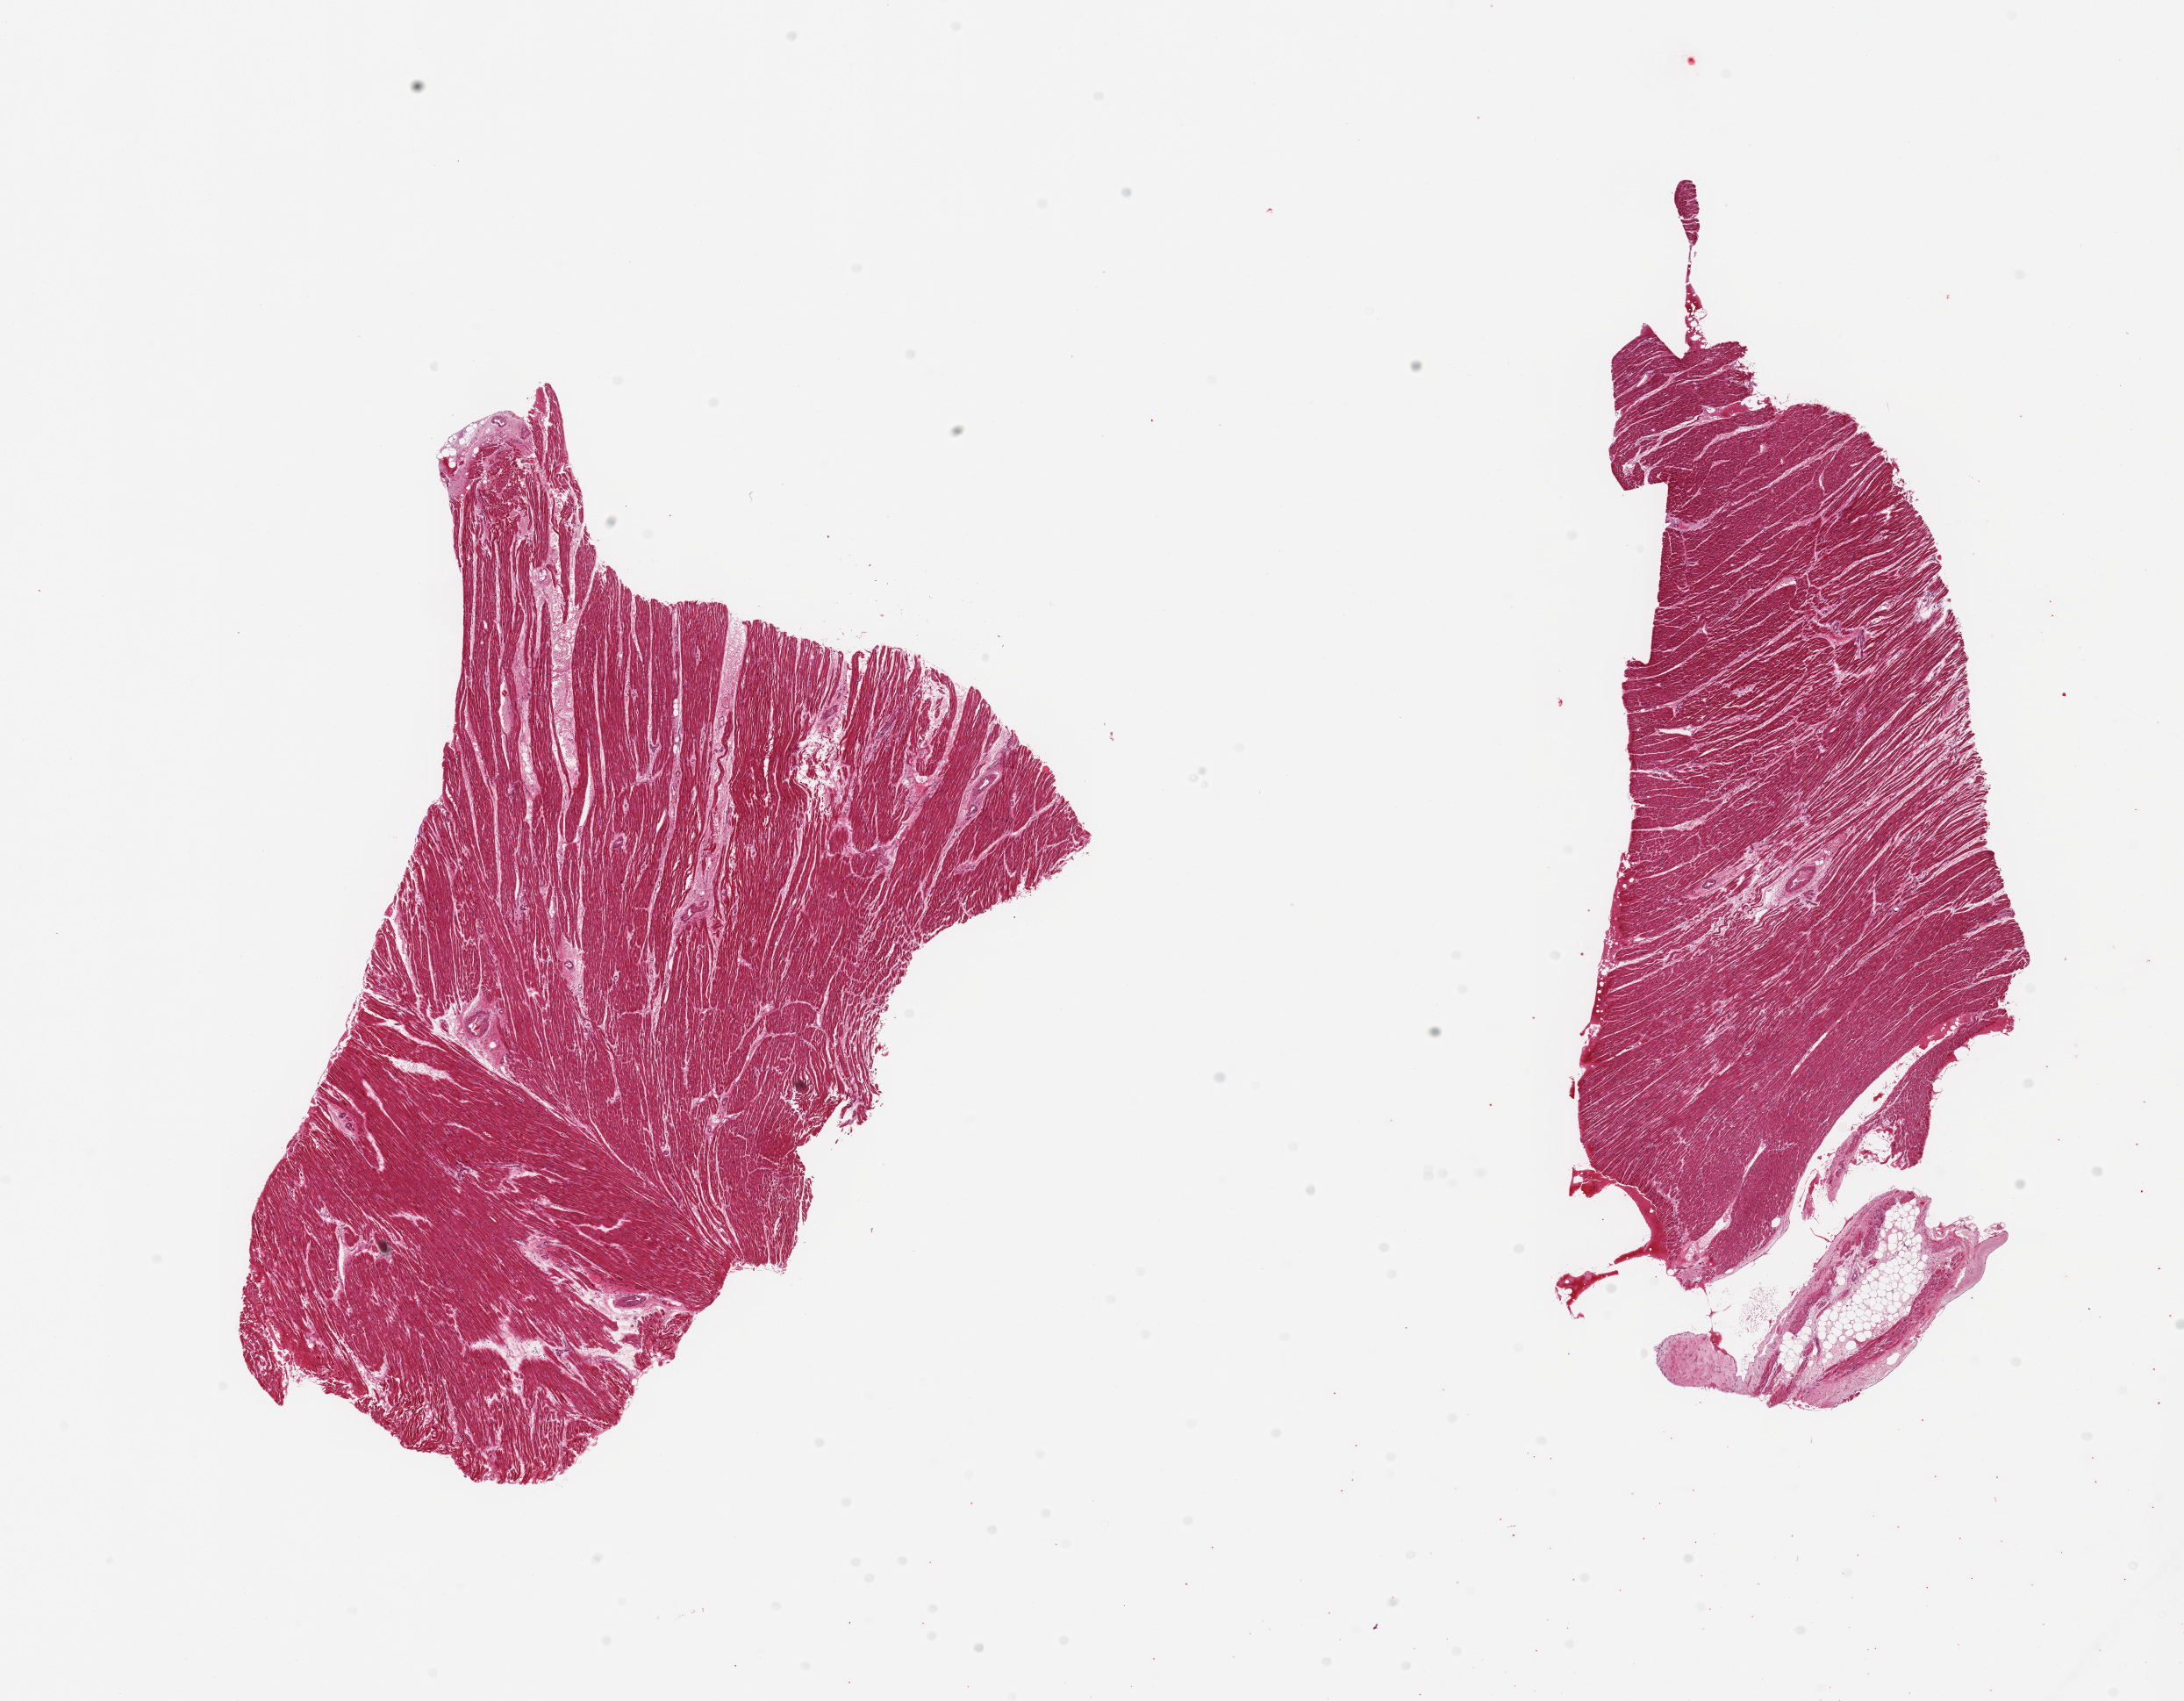
H&E whole-slide image — shown as a low-resolution overview of the whole scanned area (about 19.7 x 15.3 mm); PAXgene-fixed paraffin-embedded (PFPE) section; sampled site (target tissue): heart; donor tissue sample. Male donor.
Review note (as recorded): 2 pieces, minimal chronic ischemic change.